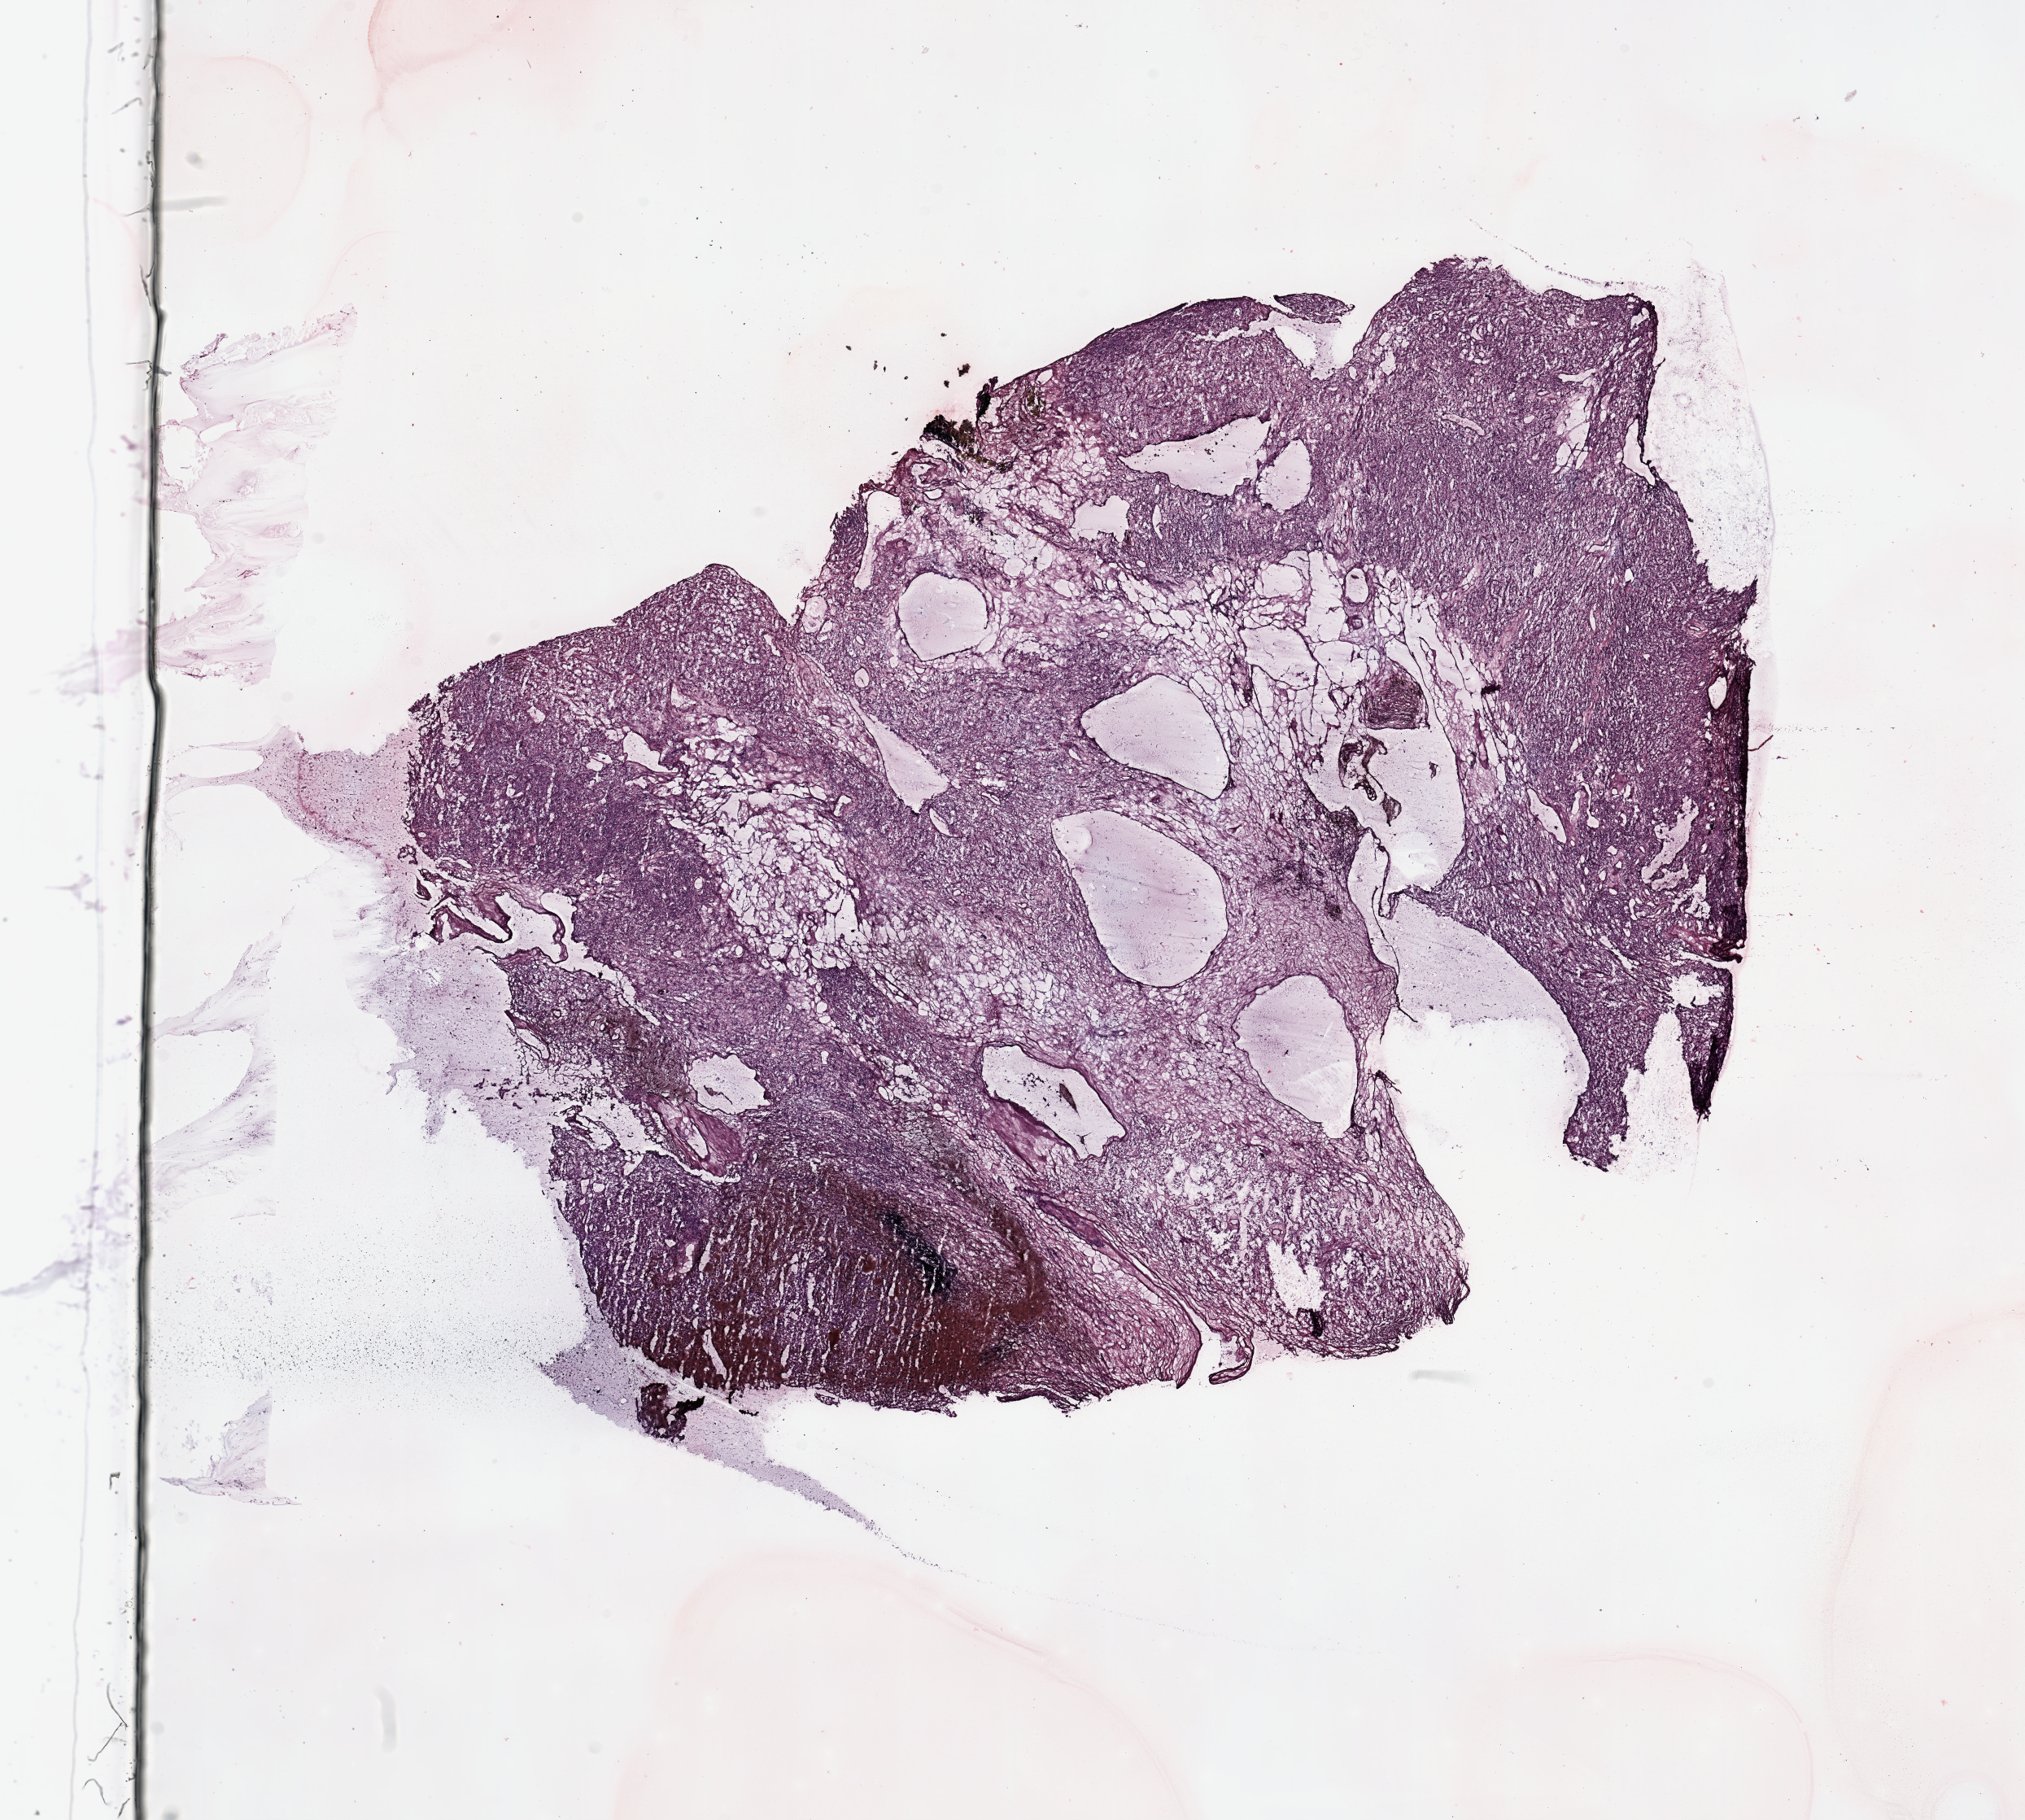
Hematoxylin and eosin (H&E) stained whole-slide image — shown as a low-resolution overview of the whole scanned area (about 19.7 x 17.7 mm, slide scanned at 20x). Tumour tissue sample, sampled site: kidney. Male, 58 y/o. Histologic grade: G2 (moderately differentiated). Composition of this section per pathologist review: tumour nuclei 80%, necrosis 15%.
Primary tumour site (as recorded): upper pole. Histologic diagnosis: Renal cell carcinoma, NOS. AJCC pathologic stage: IV.